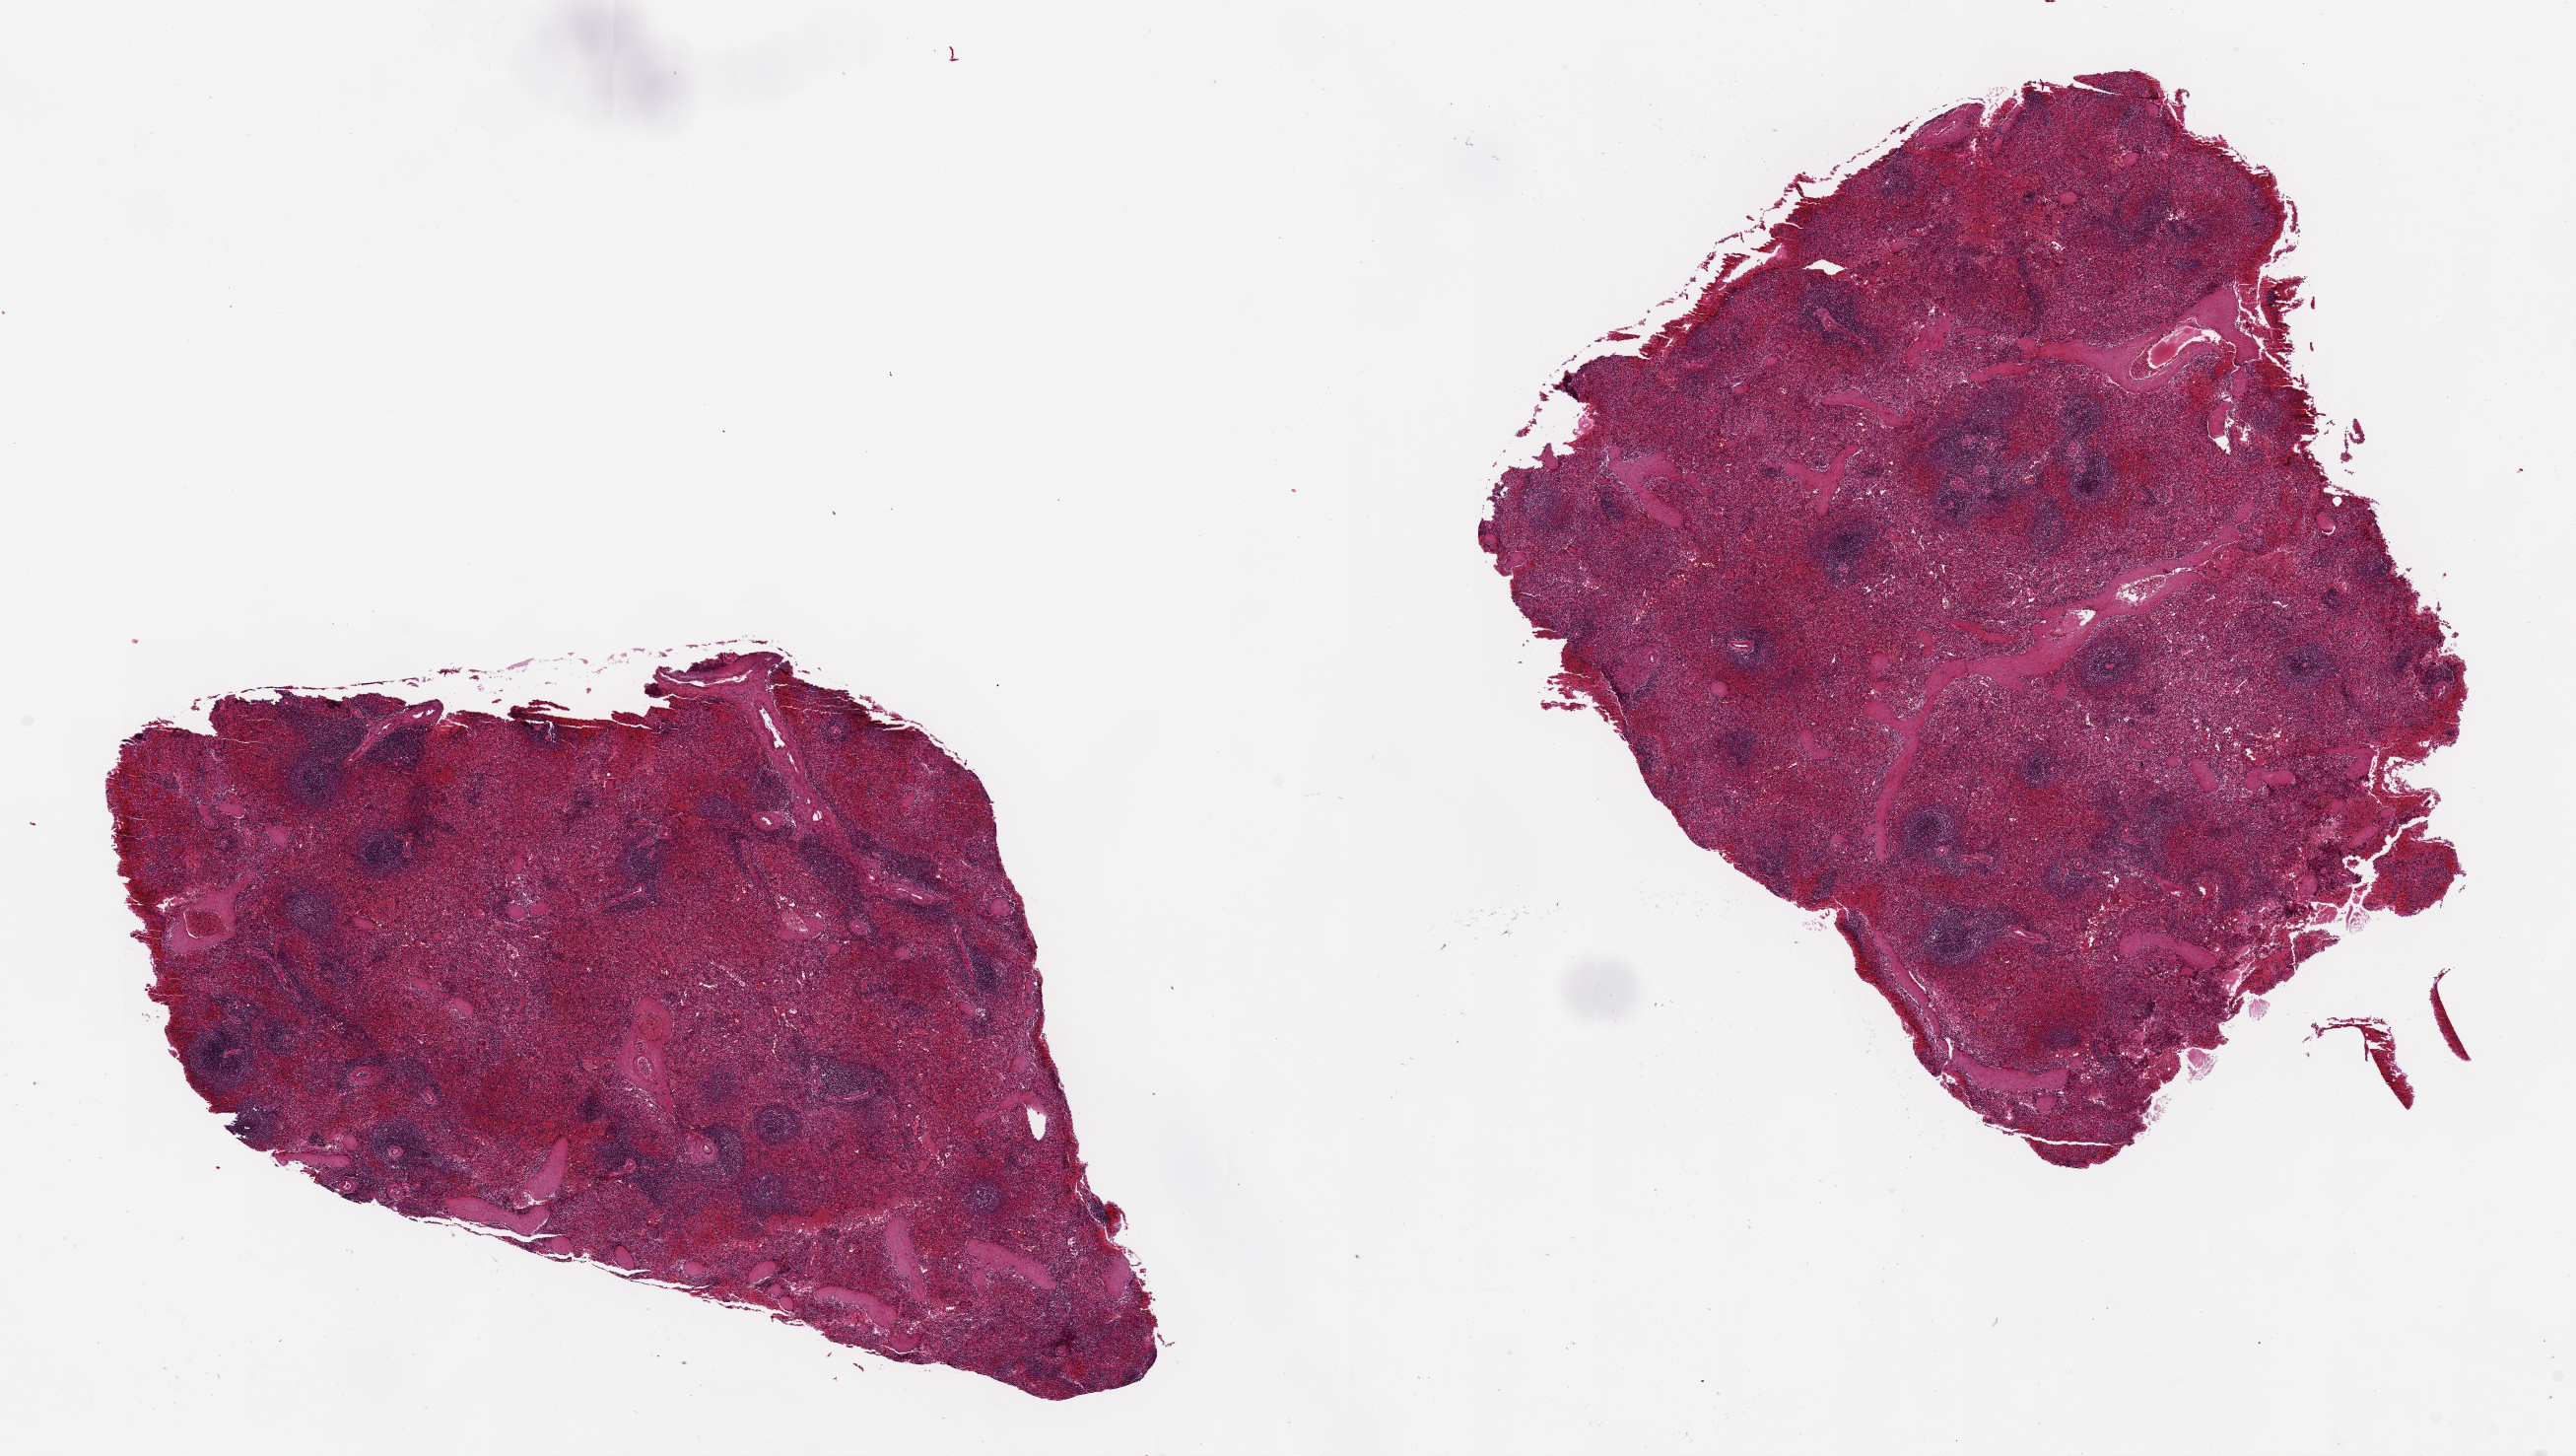
Digitized H&E-stained section — shown as a low-resolution overview of the whole scanned area (about 20.7 x 11.7 mm, from a 20x scan), PAXgene-fixed, paraffin-embedded tissue, sampled site (target tissue): spleen, donor tissue sample. Donor sex: female.
• pathologist's review note for this sample: 2 aliquots, ~9x7mm